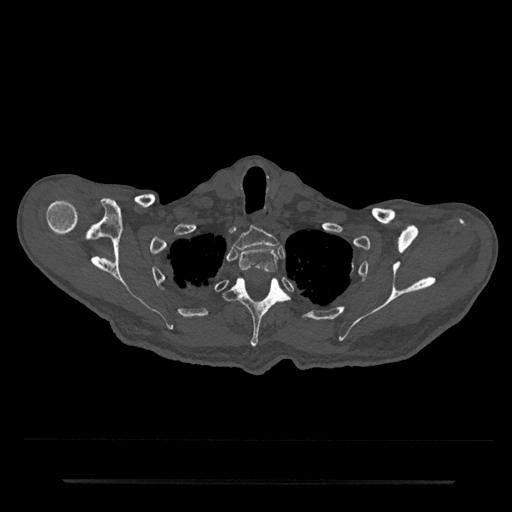
CT including the spine, one axial slice; slice 675 of 797 in the series (ordered by position); reconstruction kernel Br40s/3; bone window (W 1800 / L 400 HU); 0.5 mm slice thickness; 512 × 512 image matrix, field of view 427 × 427 mm. Patient: male, 74 years. From the clinical record (not read from this slice): primary cancer: prostate.
Outlined on this slice (semi-automatic segmentation, software-assisted and operator-edited):
- T1 vertebra: box from (x=233, y=227) to (x=279, y=250) px
- T2 vertebra: (x=239, y=248)–(x=278, y=274)
- T3 vertebra: (x=224, y=277)–(x=289, y=347)